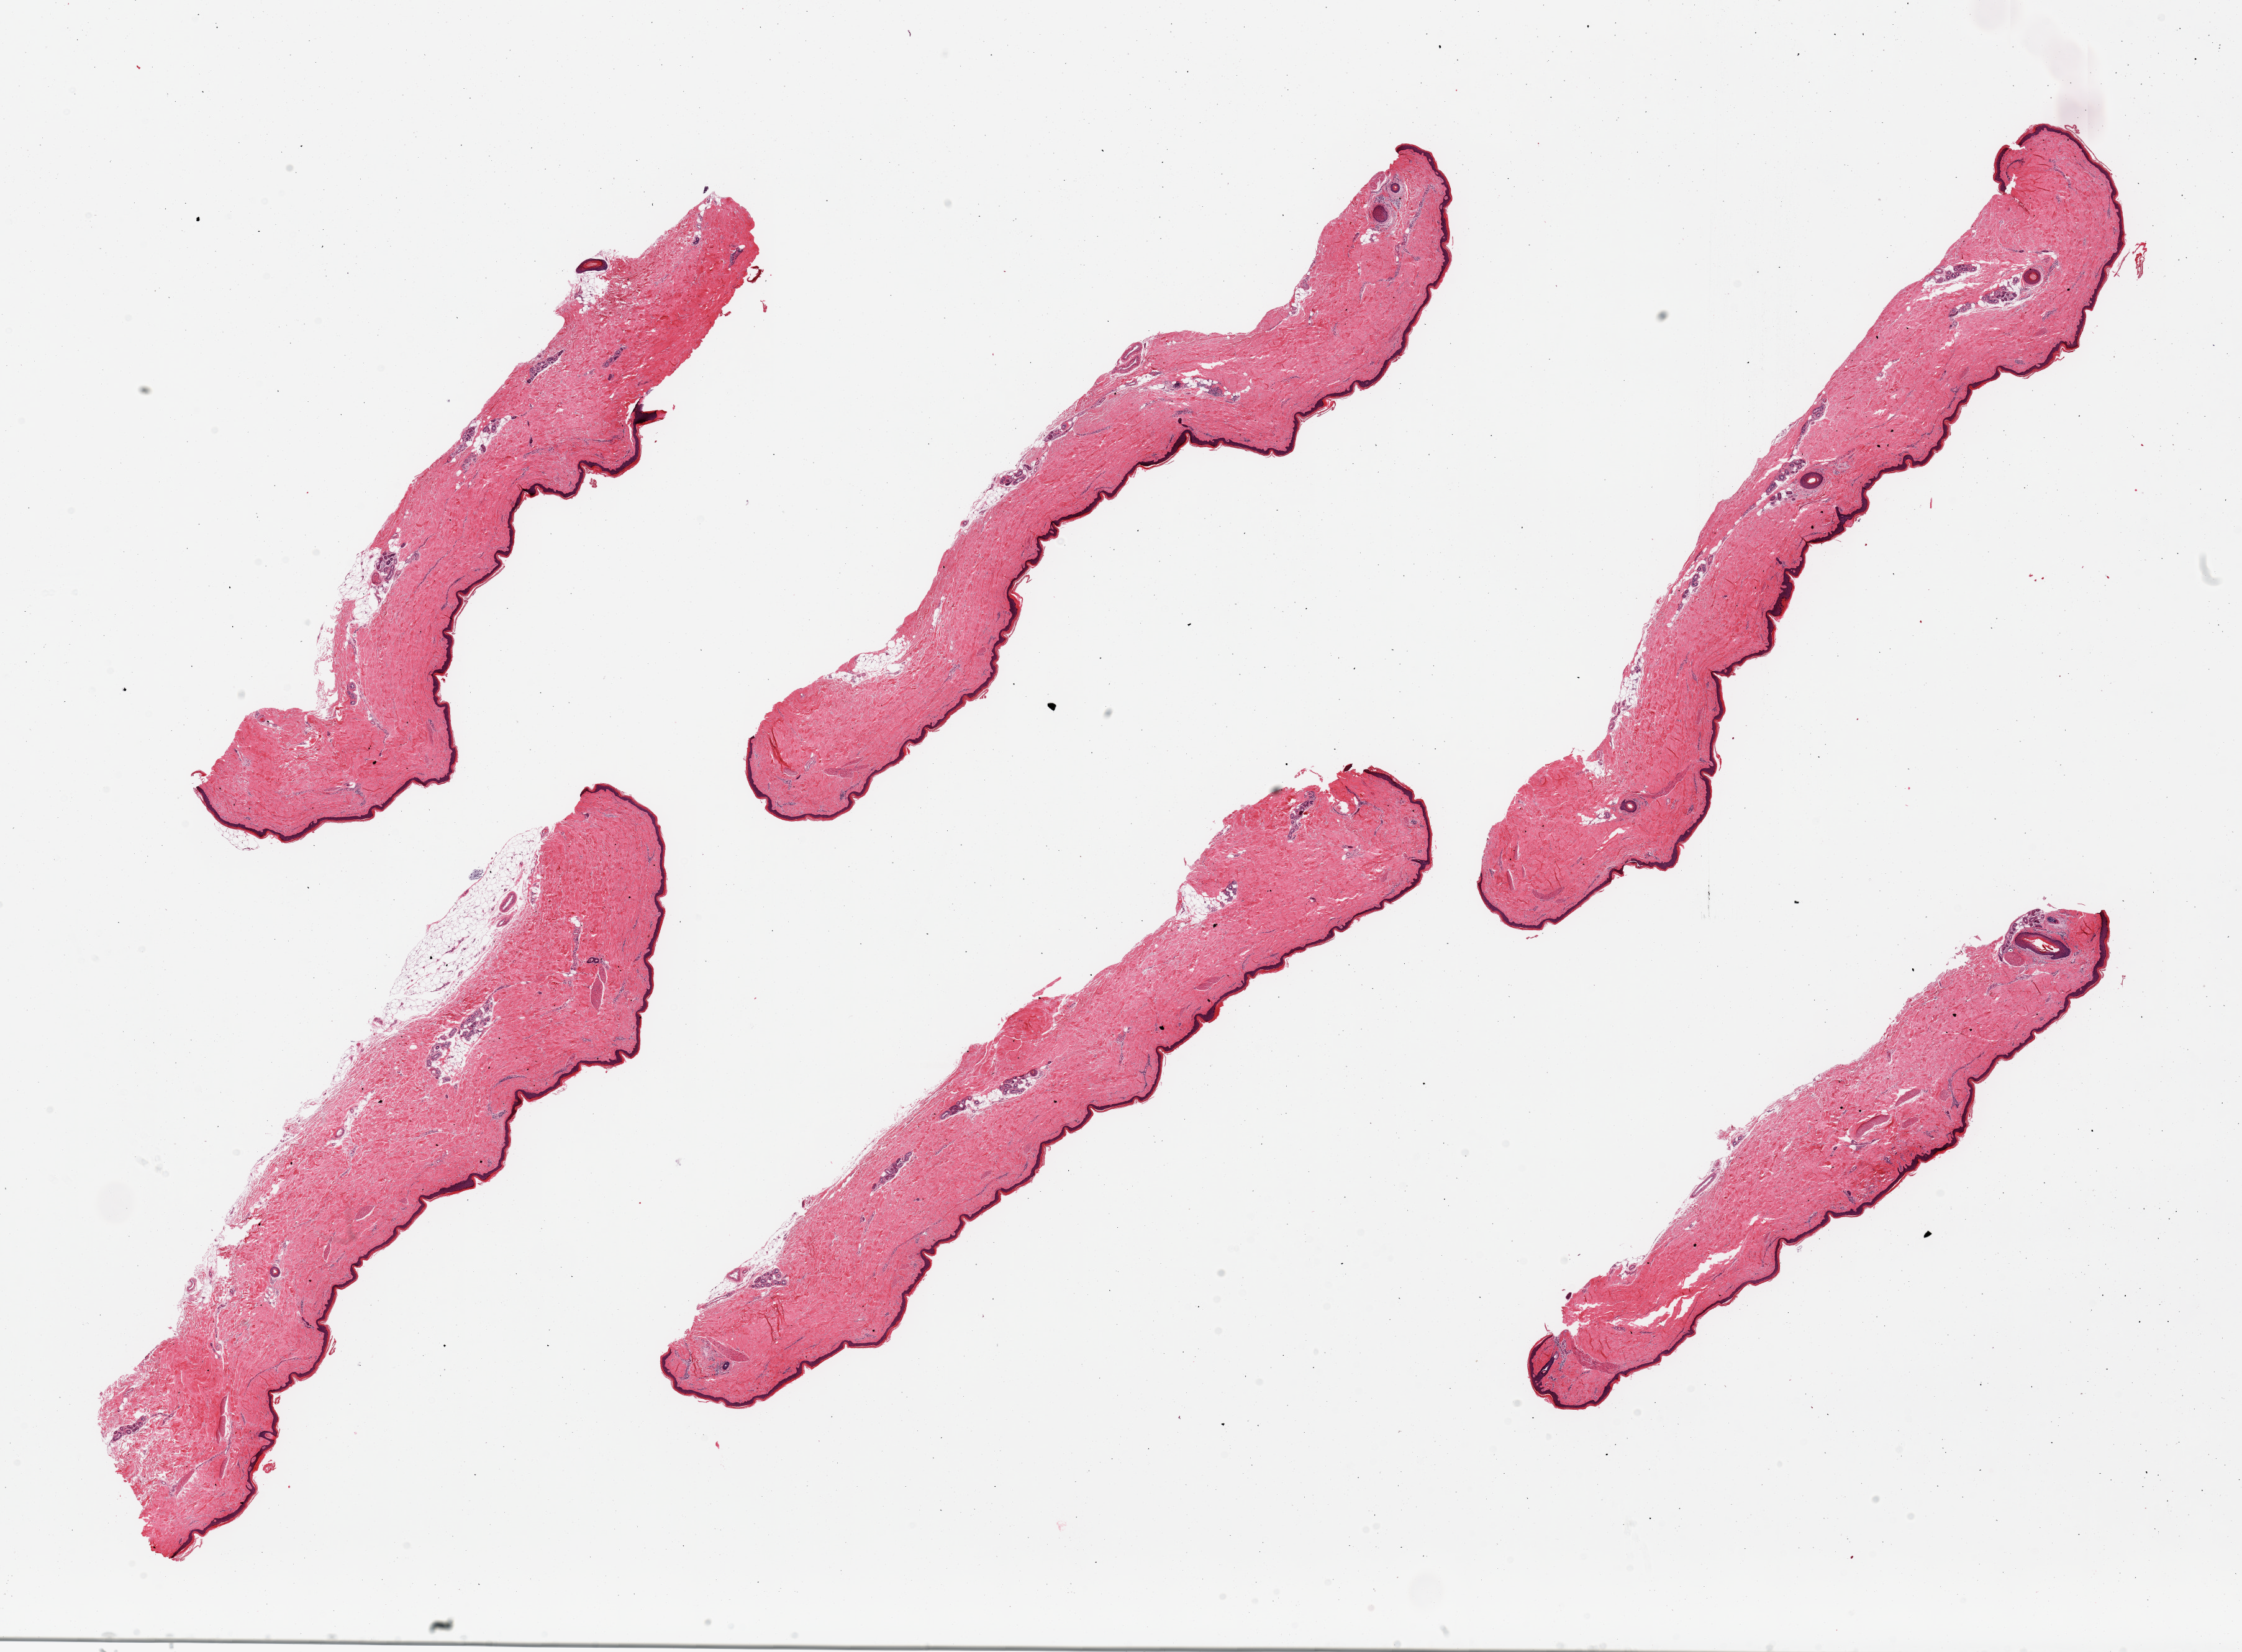
H&E whole-slide image, shown as a low-resolution overview of the whole scanned area (about 28.5 x 21.0 mm); PAXgene-fixed paraffin-embedded (PFPE) section; section of skin of lower leg (target tissue); tissue donor sample.
- review note (as recorded): 6 pieces, trace adherent dermal fat; squamous epithelium is ~50 microns